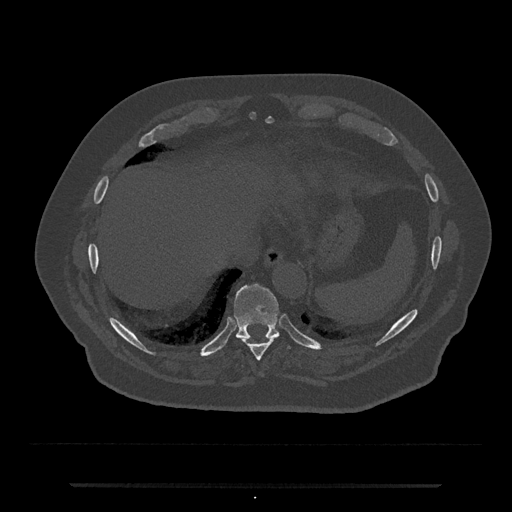
CT including the spine, one axial slice. Position 732 of 797 along the scan axis. Reconstruction kernel Br40s/3. 120 kVp. Bone window (W 1800 / L 400 HU). 0.5 mm slice thickness. 512 × 512 image matrix. Patient: male, 80 years. From the clinical record (not read from this slice): primary cancer: prostate.
Structures marked on this image (semi-automatically segmented with operator editing):
- T10 vertebra: bounding box [x1, y1, x2, y2] px = [234, 284, 290, 349]
- T9 vertebra: [241, 338, 276, 361]